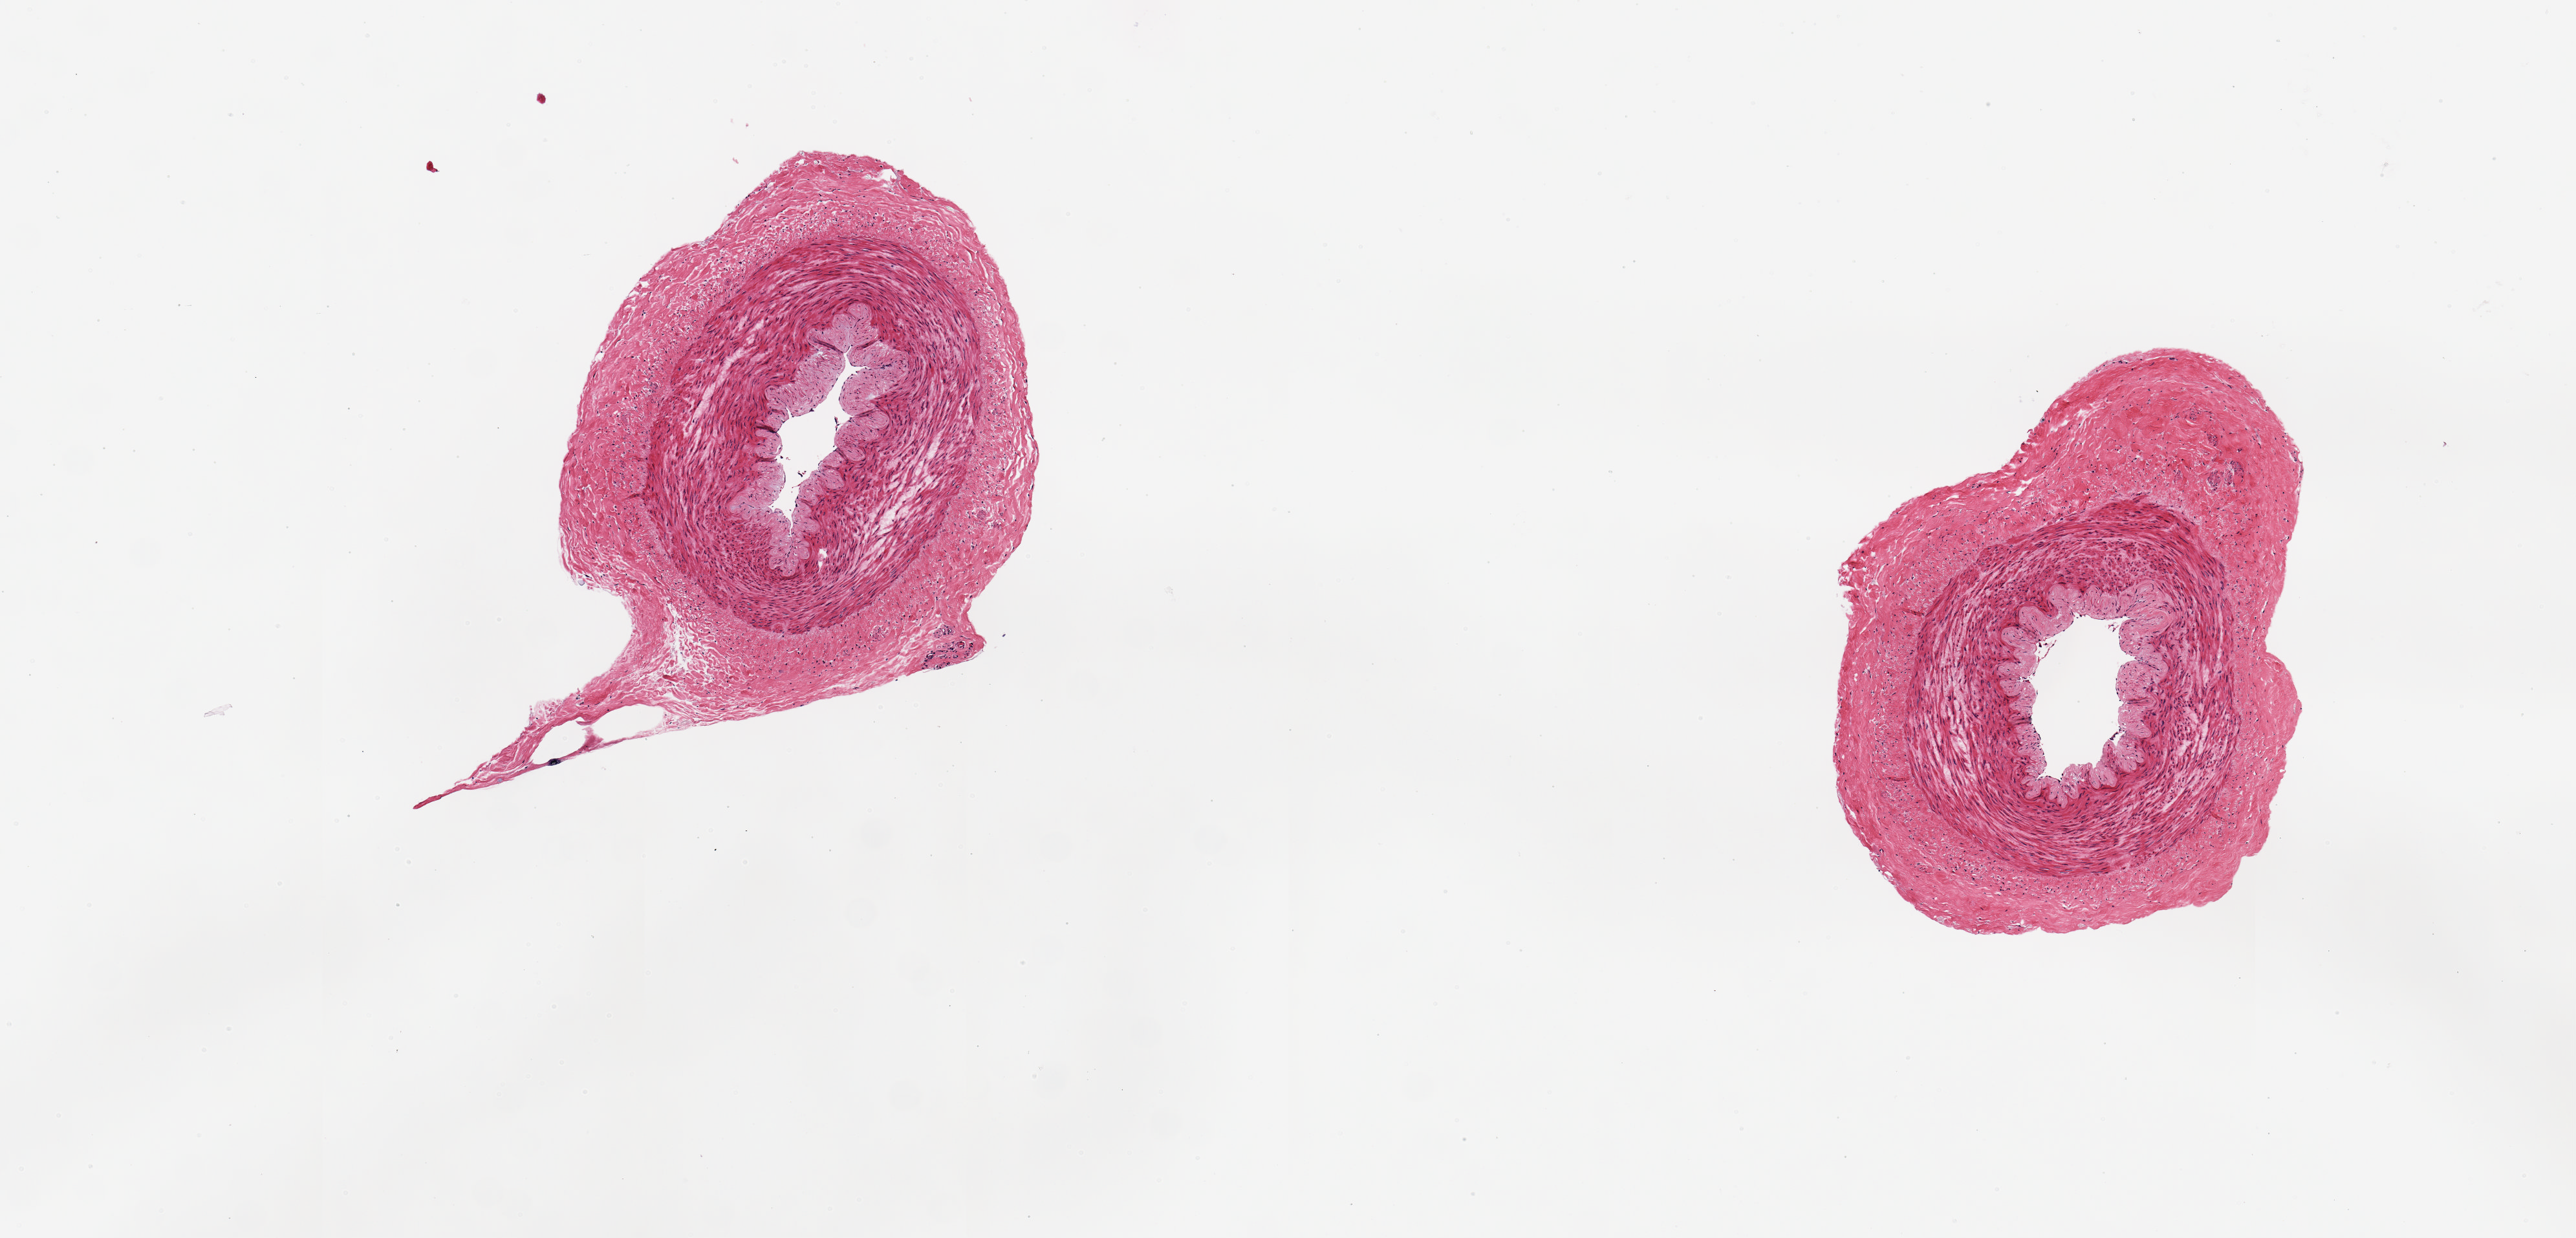
Whole-slide image, hematoxylin and eosin (H&E) stain, brightfield — shown as a low-resolution overview of the whole scanned area (about 7.9 x 3.8 mm, slide scanned at 20x); PAXgene-fixed paraffin-embedded (PFPE) section; section of tibial artery (target tissue); donor tissue sample.
Pathologist's review note for this sample: 2 ~ 1.5d aliquots, good clean specimens.